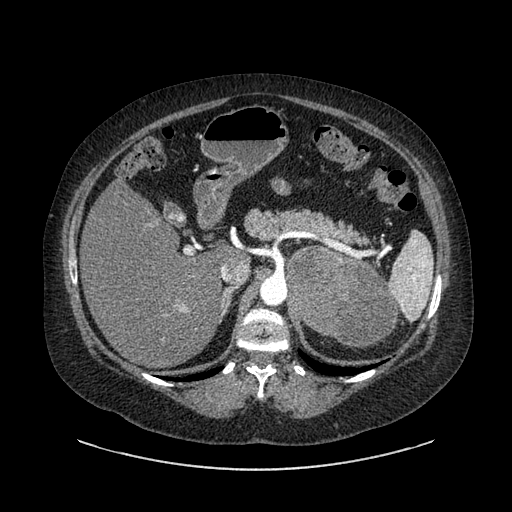
Contrast-enhanced abdominal CT, one axial slice; position 588 of 769 along the scan axis; 120 kVp; soft-tissue window (W 400 / L 40 HU); 0.62 mm slice thickness; 512 × 512 image matrix, field of view 460 × 460 mm. Female patient, age 61 years. From the clinical record (not read from this slice): diagnosis: adrenocortical carcinoma; tumour side: left adrenal.
Annotated regions visible in this slice (semi-automatic segmentation, software-assisted and operator-edited):
- mass: box from (x=288, y=248) to (x=396, y=345) px